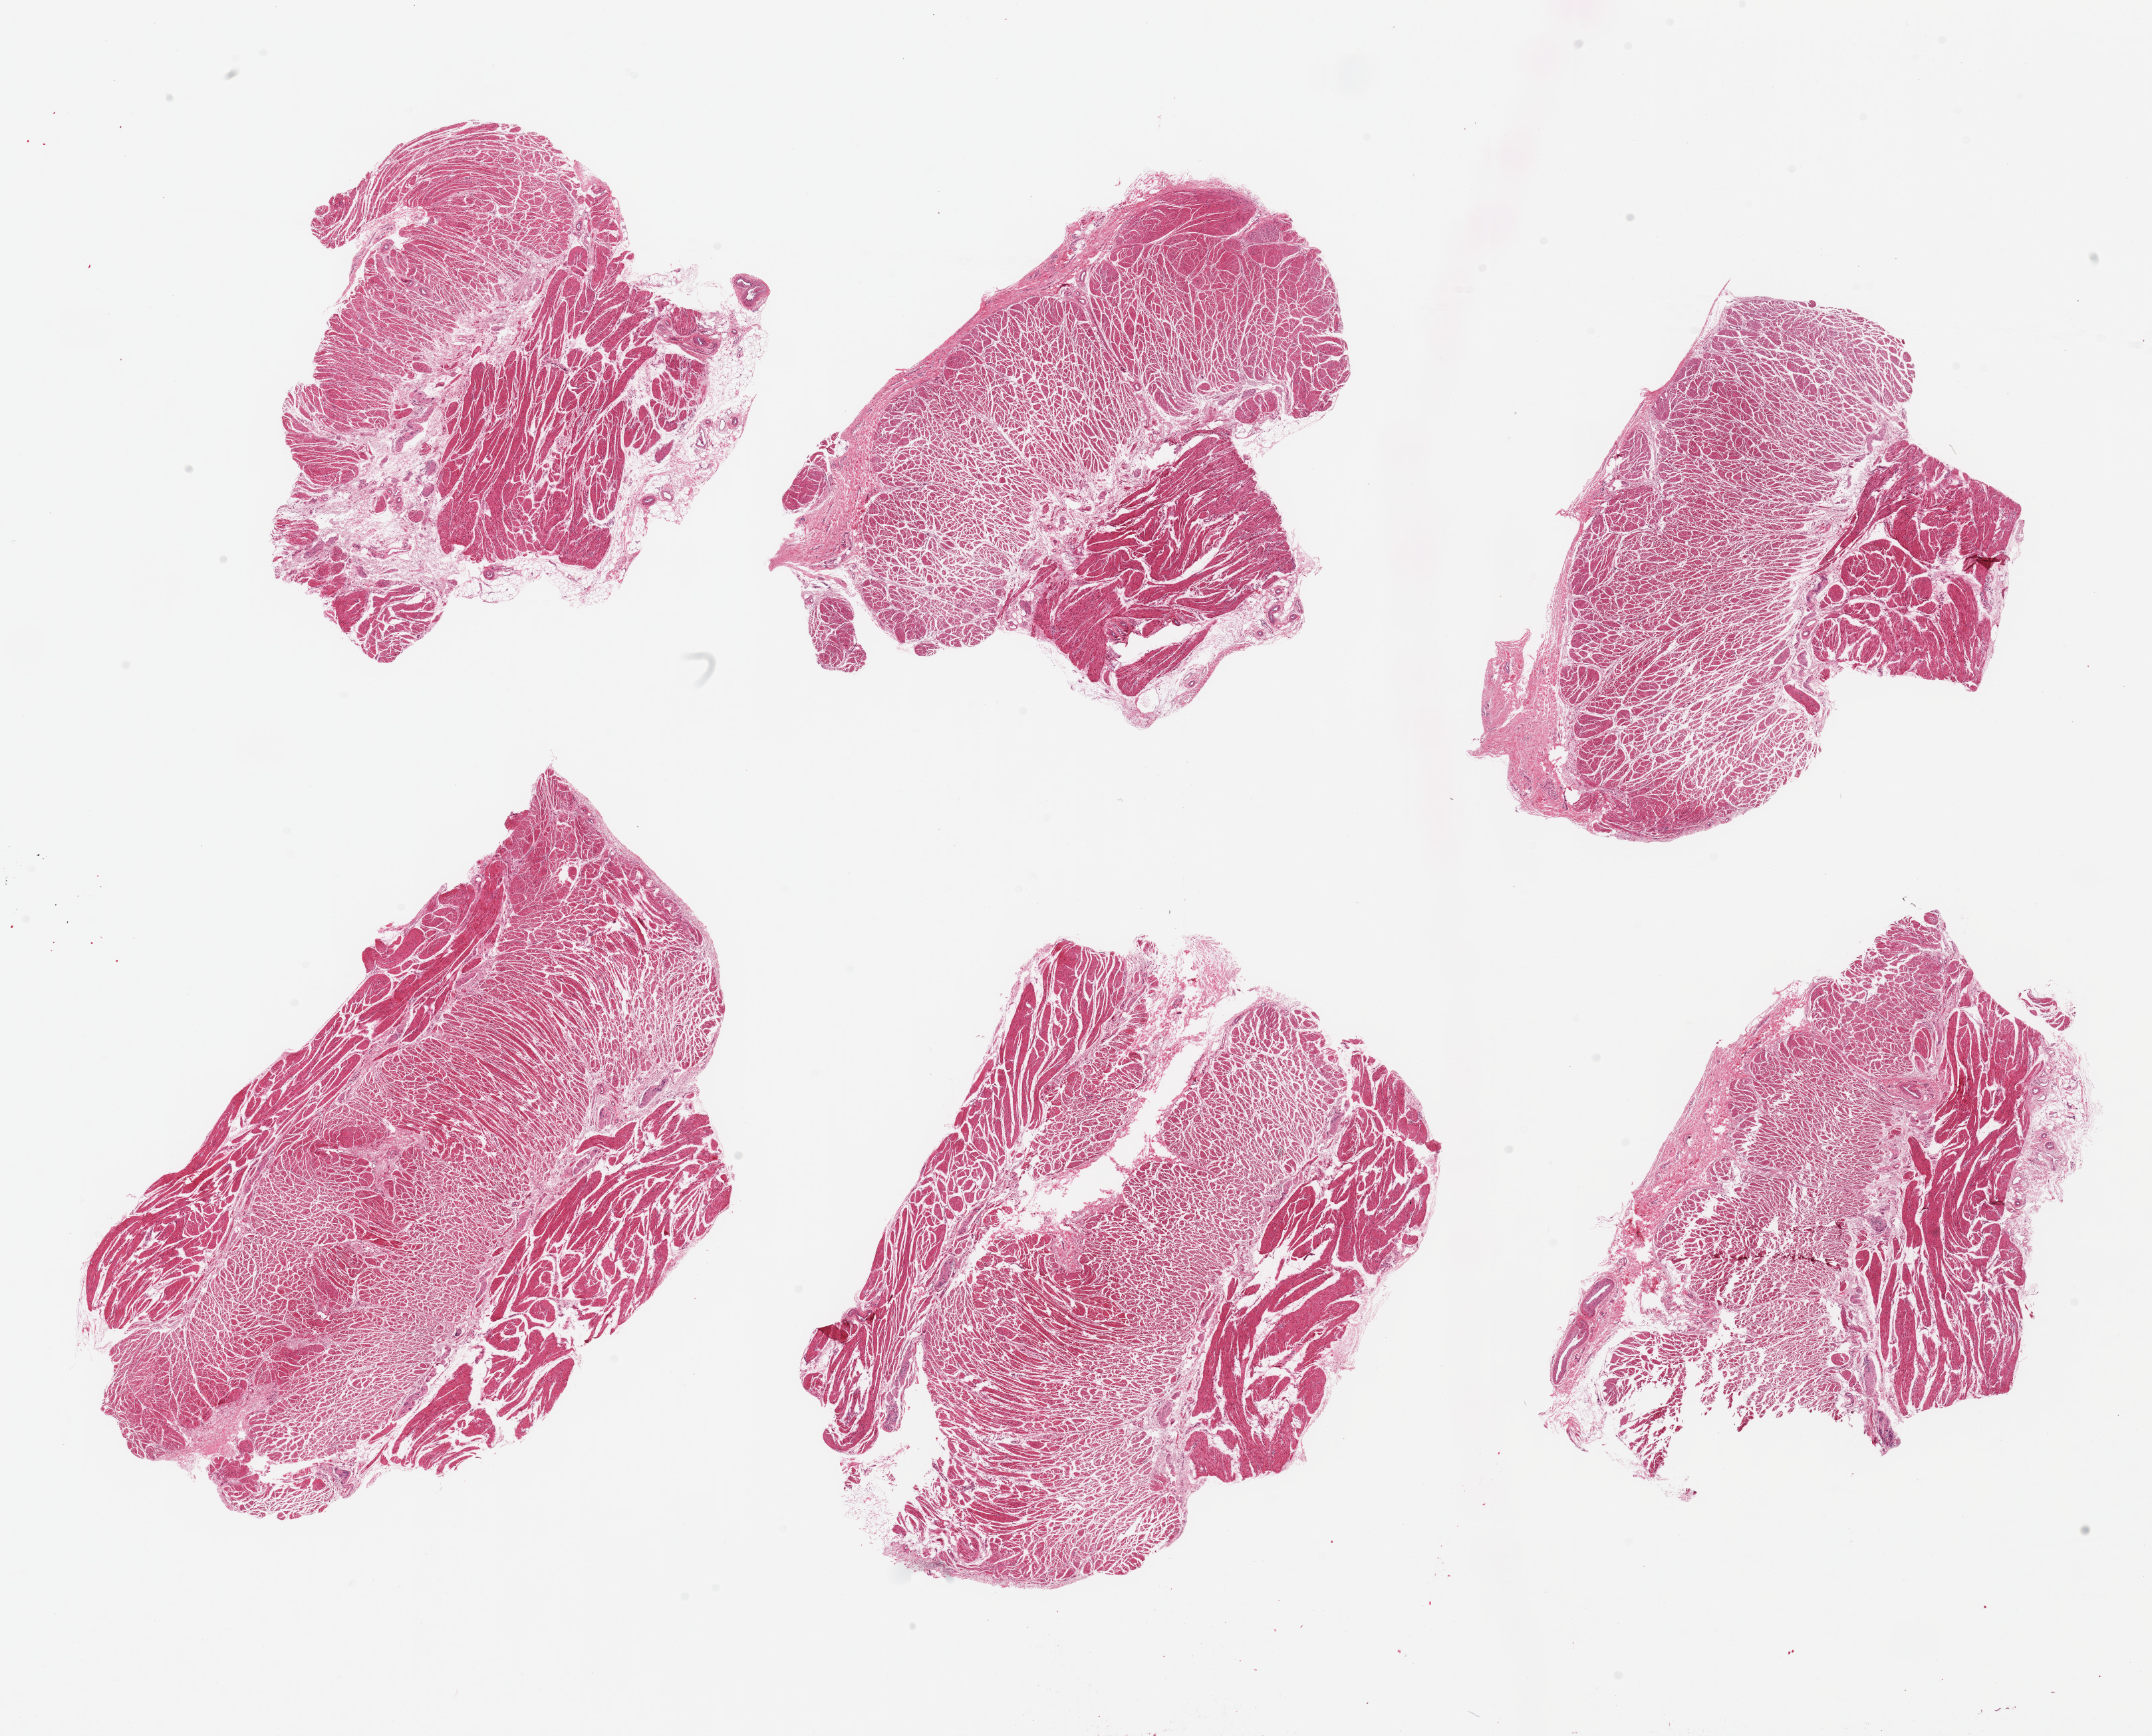
Digitized haematoxylin and eosin-stained section, brightfield, whole scanned area (about 25.6 x 20.6 mm, acquisition: 20x scan) shown as a low-resolution overview. PAXgene-fixed paraffin-embedded (PFPE) section. Target tissue: gastroesophageal junction. Donor tissue sample. Donor sex: male.
Pathologist's review note for this sample: 6 pieces, confirmed target muscularis.